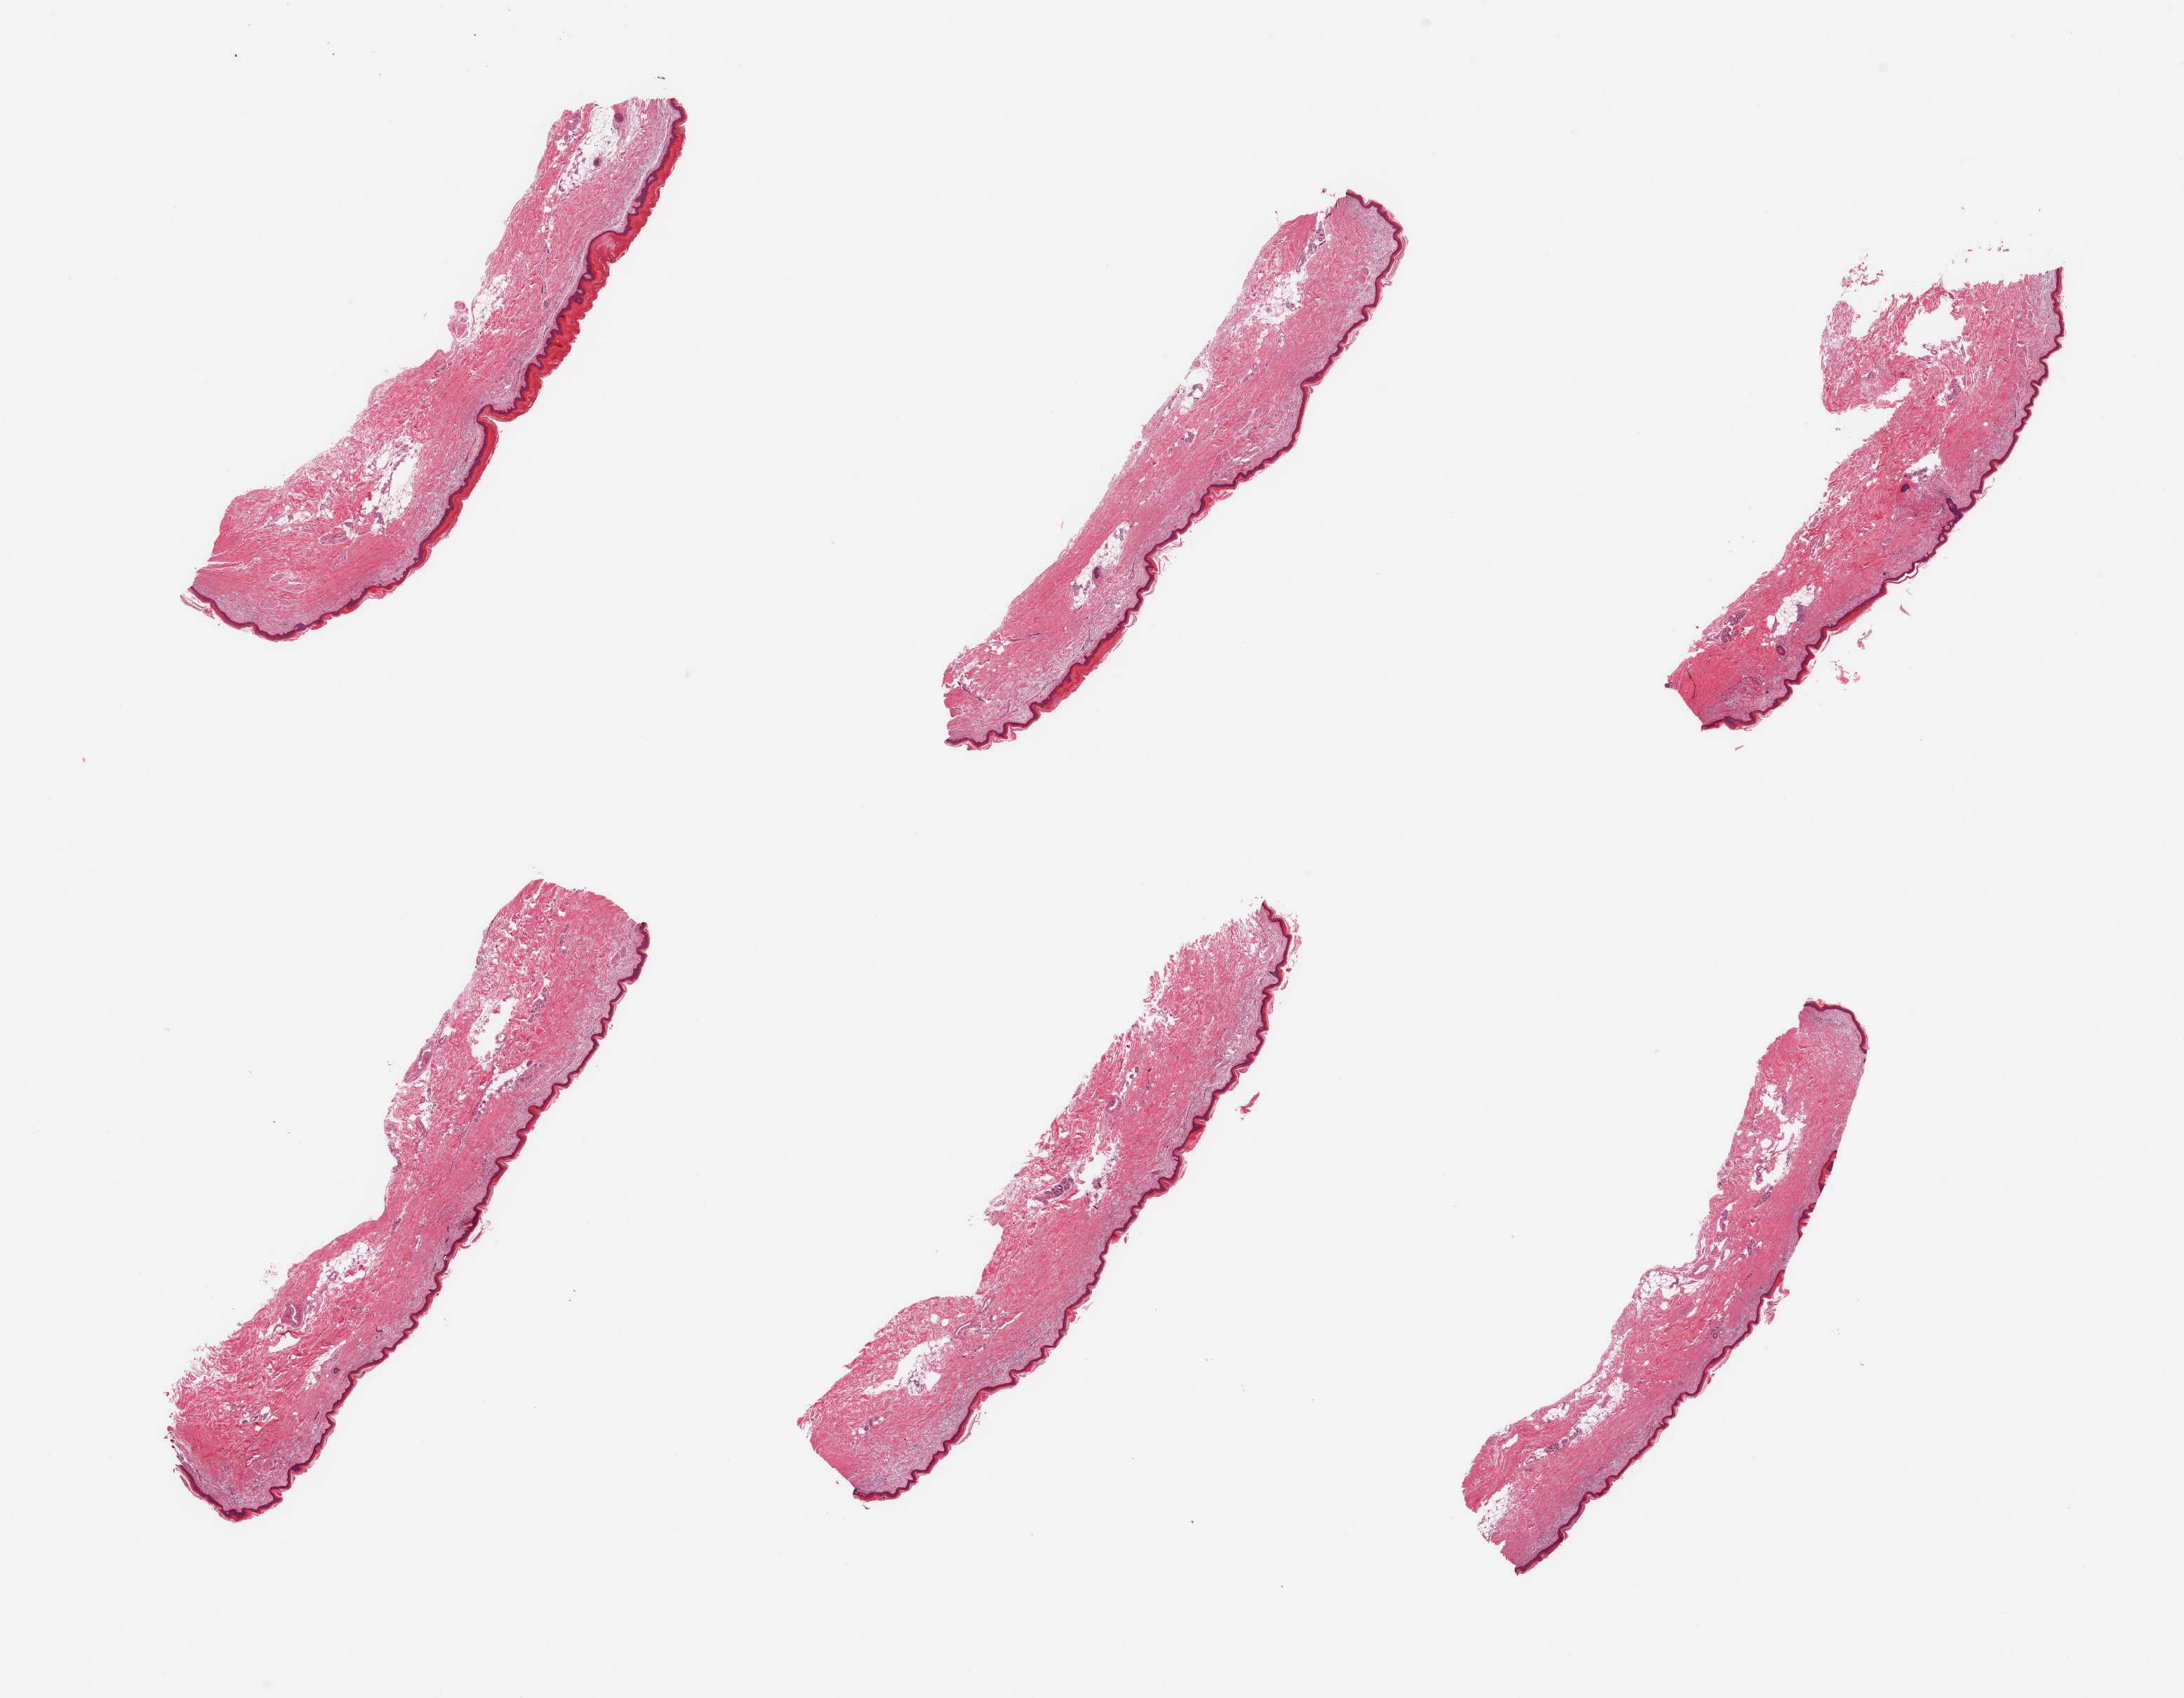
Digitized hematoxylin and eosin (H&E)-stained section, brightfield, a low-resolution overview of the entire scanned area, about 24.6 x 19.1 mm (from a 20x scan). PAXgene-fixed paraffin-embedded (PFPE) section. Target tissue: skin of lower leg. Tissue donor sample. Female donor.
Pathologist's review note for this sample: 6 pieces; includes up to ~10% internal fat, epidermis measures 20 to 31 microns, hyperkeratosis, solar elastosis.